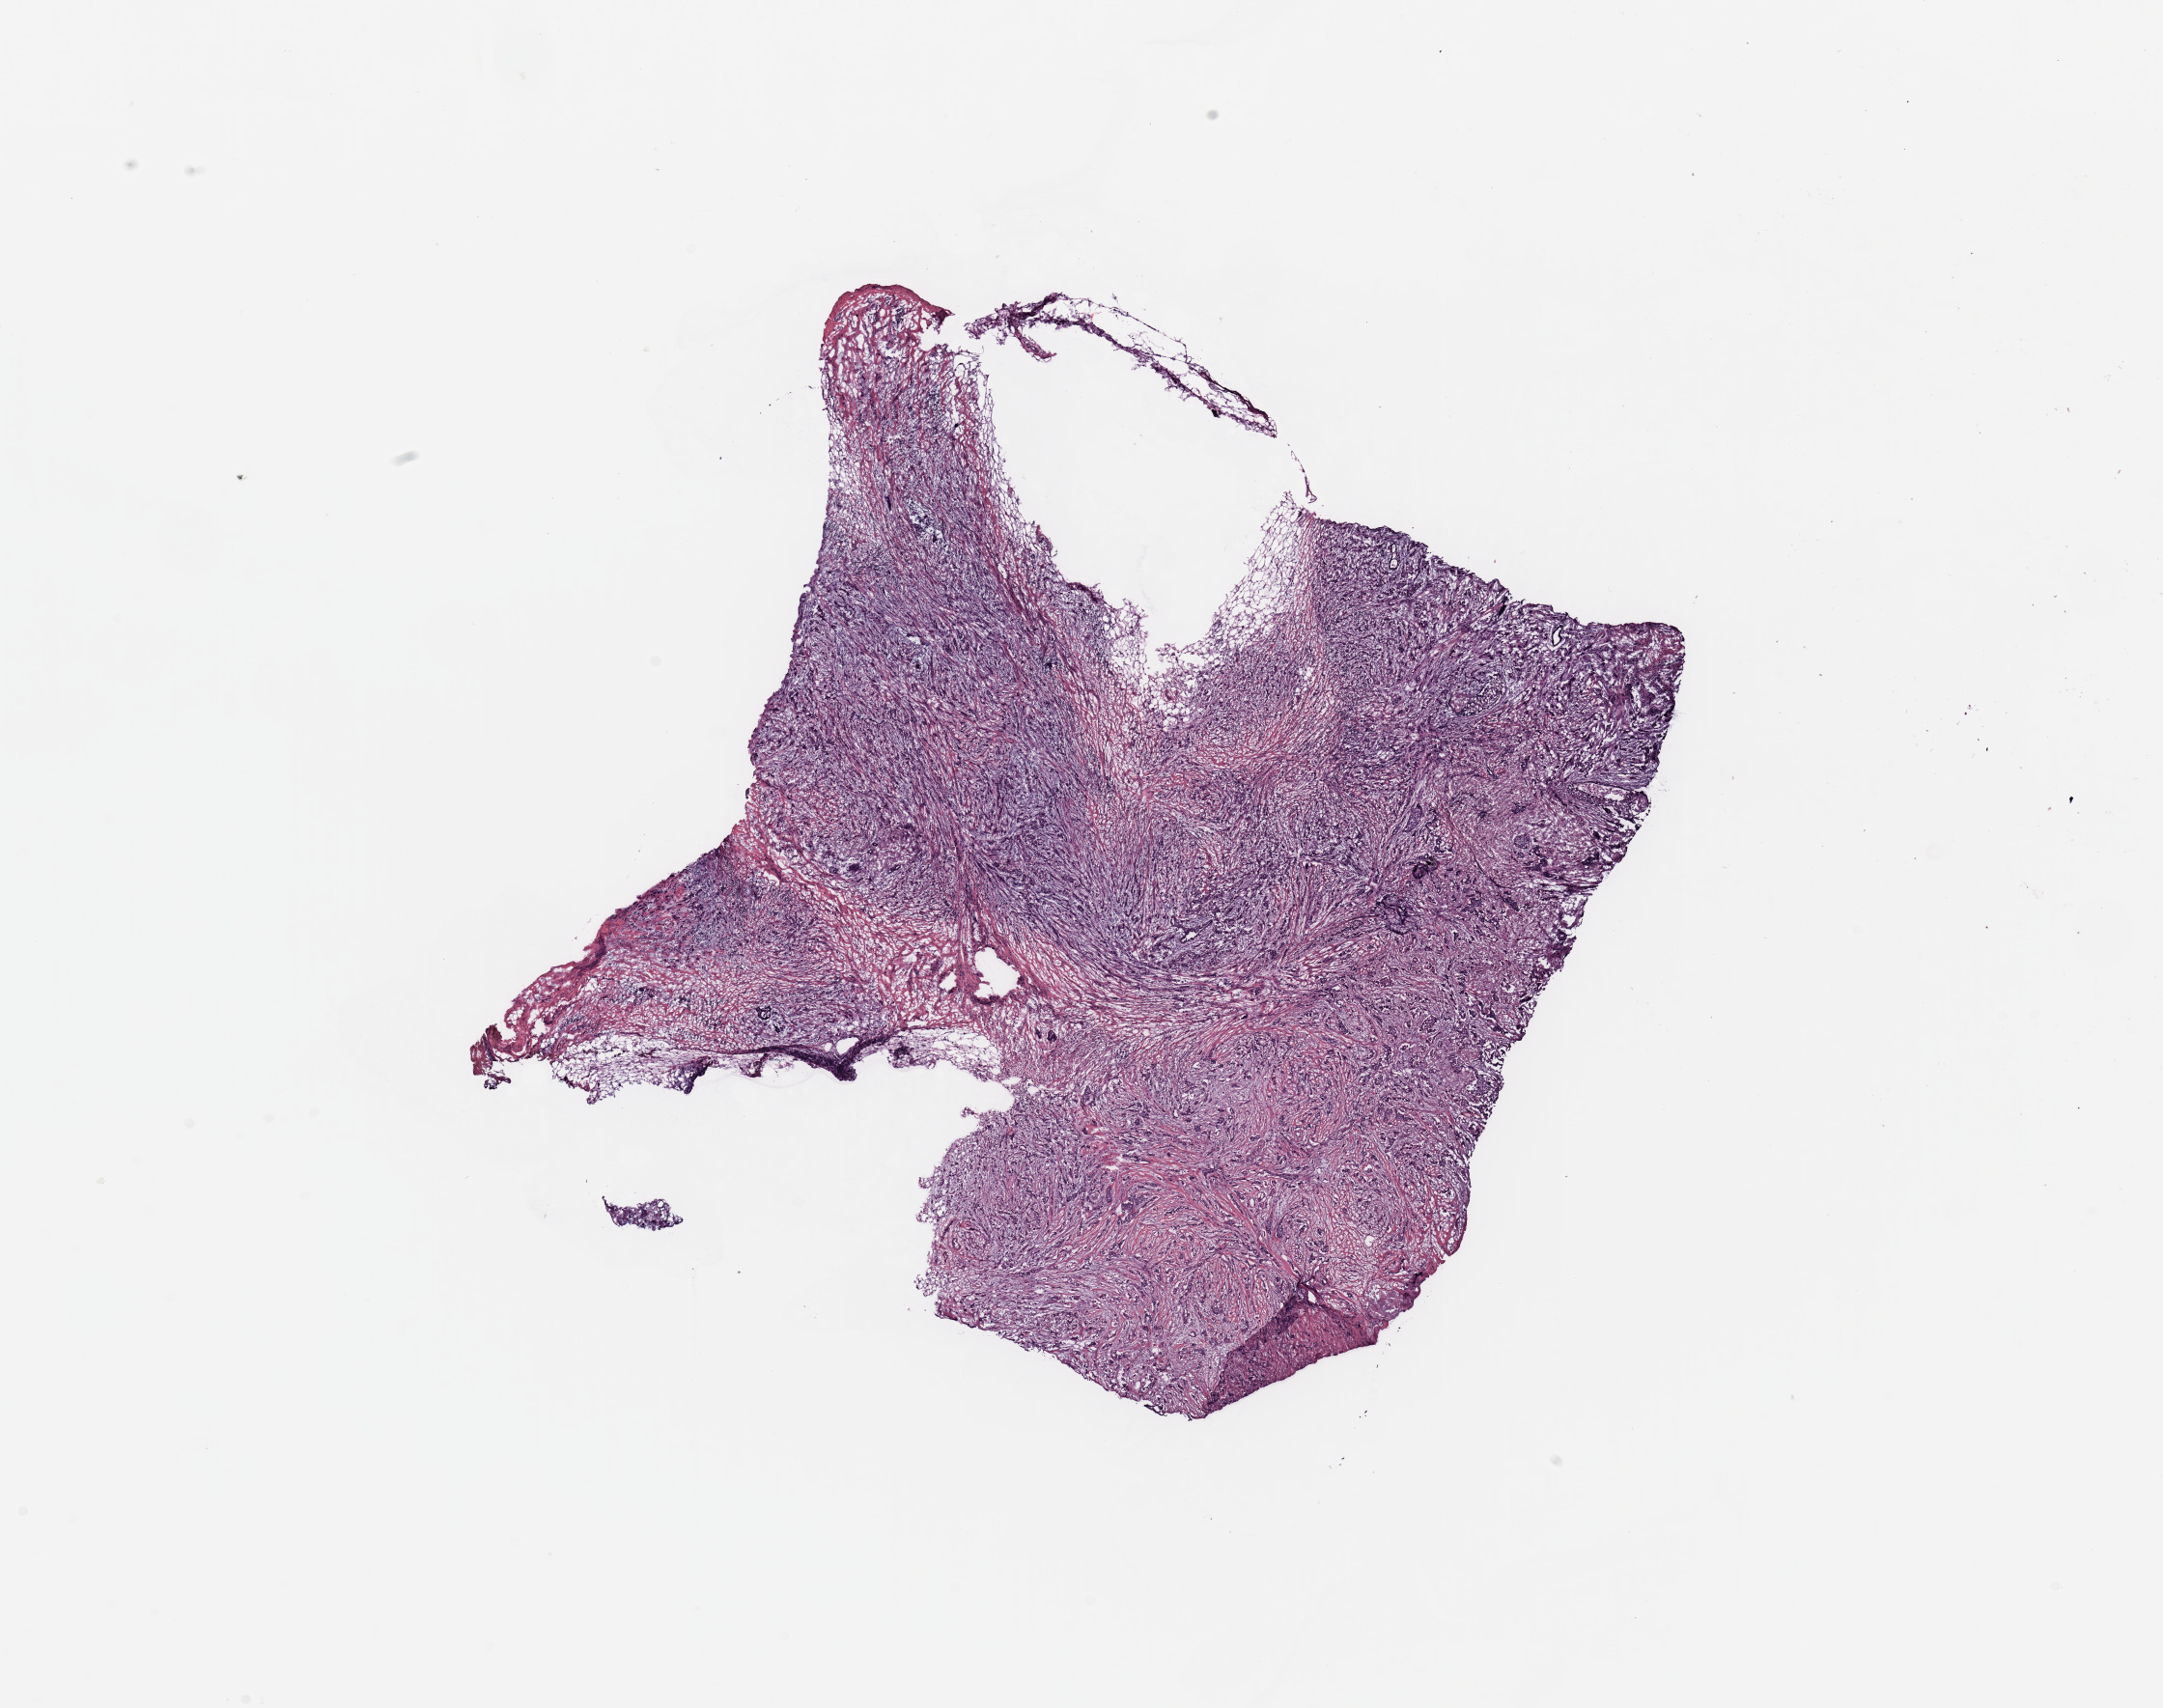
Whole-slide histology image, H&E-stained — low-resolution overview of the scanned area, about 17.7 x 14.0 mm. Breast, tissue type not recorded.
Patient diagnosis (cohort enrolment): breast cancer (breast).